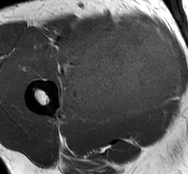
MRI of an extremity soft-tissue mass, one axial slice. Position 41 of 93 along the scan axis. MR volume resampled by the dataset authors to the PET/CT grid (not the native acquisition matrix). 3.27 mm slice thickness. 188 × 174 image matrix, field of view 184 × 170 mm. Male patient. From the clinical record (not read from this slice): histological type: undifferentiated - pleiomorphic; grade: high; site of the primary tumour: right thigh.
Structures marked on this image (expert contour drawn on MRI and transferred to this co-registered scan by the dataset authors):
- gross tumour volume including surrounding oedema: bounding box [x1, y1, x2, y2] px = [56, 19, 181, 125]
- gross tumour volume (mass): [70, 19, 181, 120]